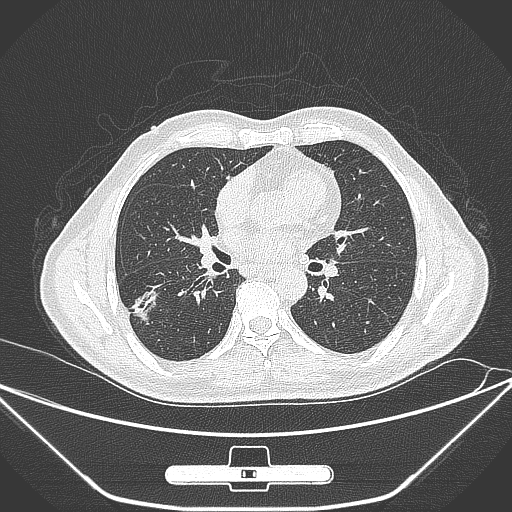
Chest CT, one axial slice. Position 145 of 309 along the scan axis. 120 kVp. Lung window (W 1500 / L -600 HU). 1 mm slice thickness. 512 × 512 image matrix, field of view 398 × 398 mm. Male patient, age 71 years. From the clinical record (not read from this slice): clinical TNM (as recorded): T1c N0 M0; histopathological grade: G2.
Structures marked on this image (bounding box drawn by a radiologist):
- lung tumour (recorded histology: adenocarcinoma): bounding box <128,284,157,327> (left, top, right, bottom; pixels)